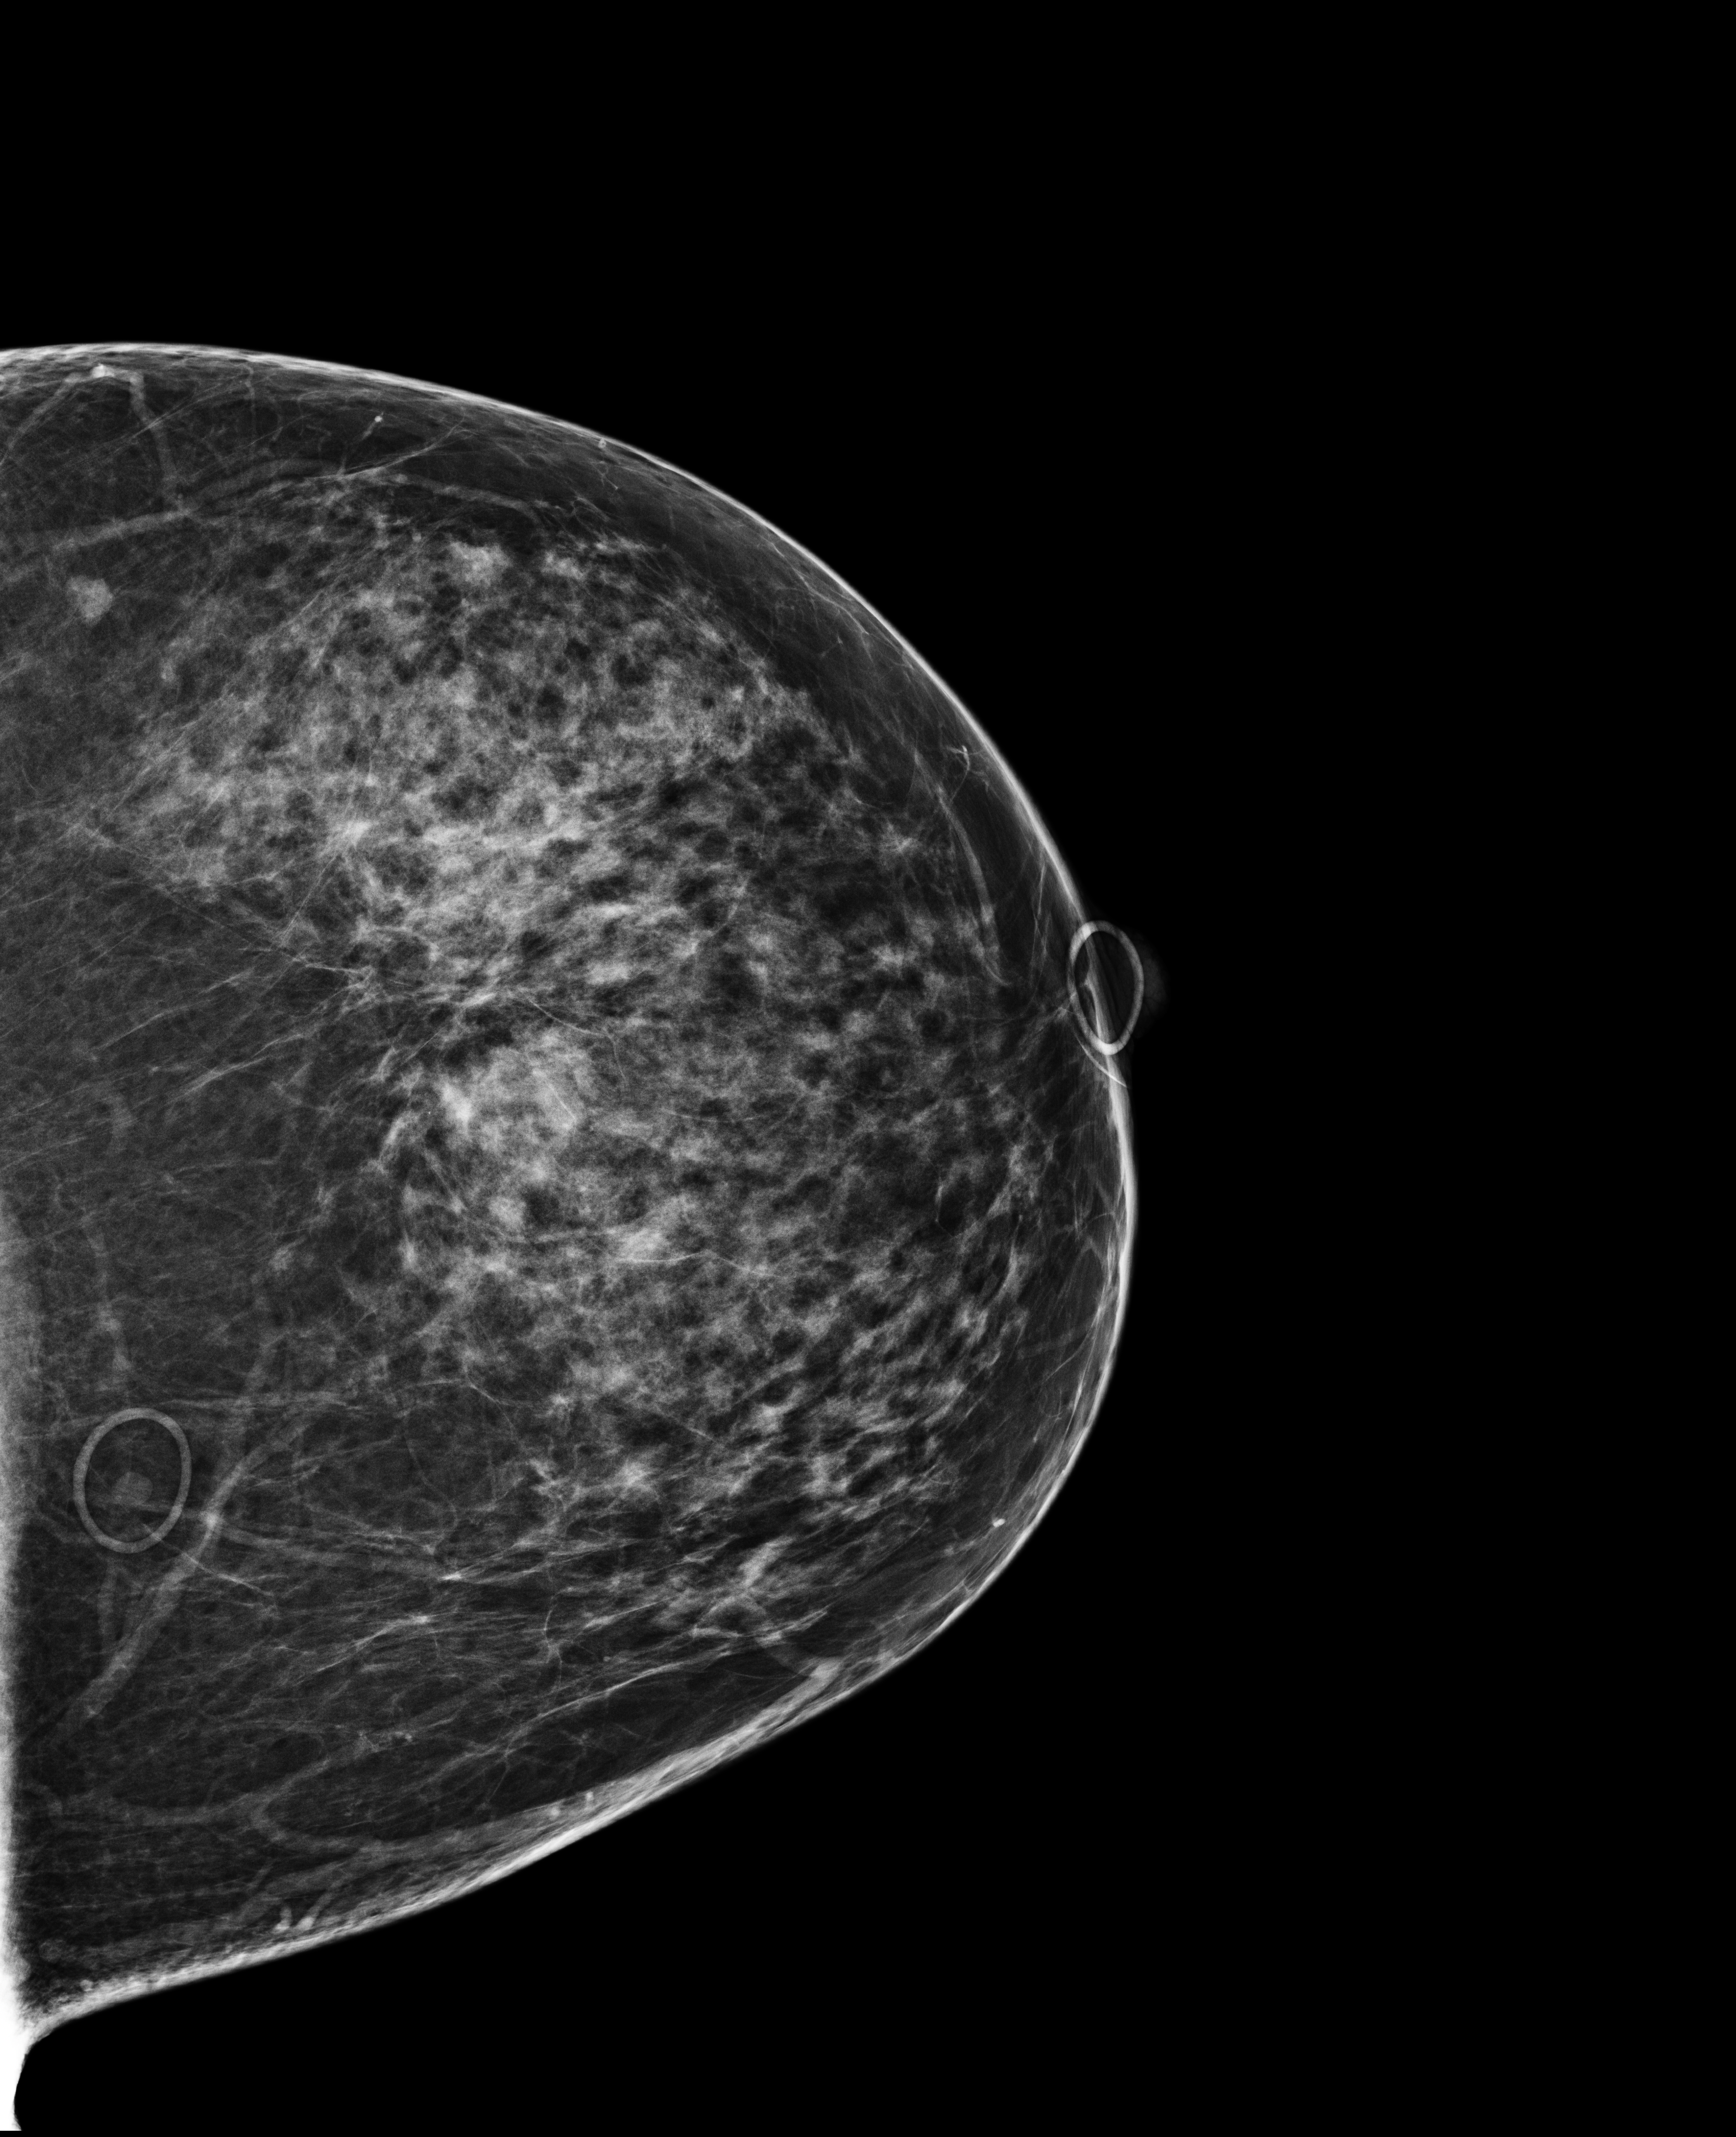
Annual screening mammography examination, compressed breast thickness 62 mm. Female patient, age 51 years.
Image type: full-field digital mammogram. Breast: left. Projection: craniocaudal (CC) view.